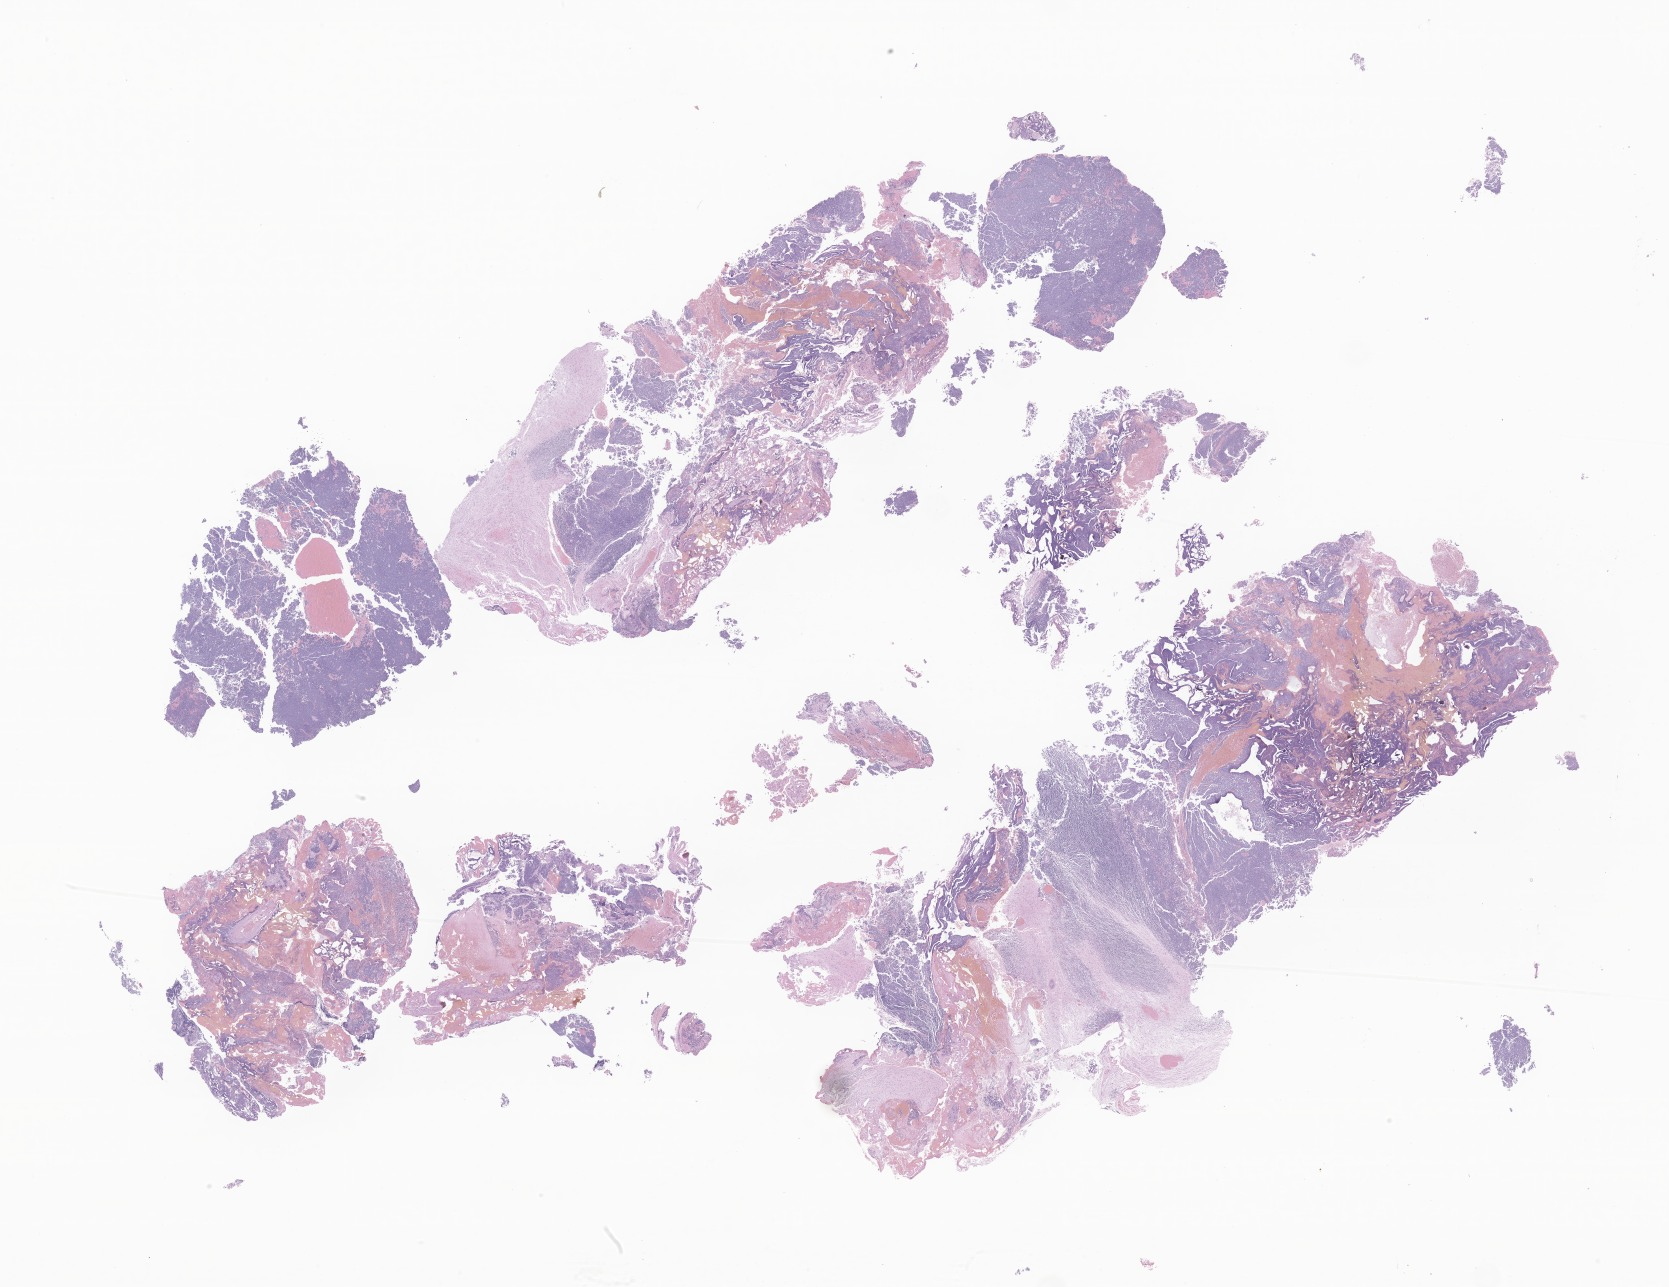
Digitized hematoxylin and eosin (H&E)-stained section of tumor tissue from the cerebellum, whole scanned area (about 28.1 x 21.7 mm) shown as a low-resolution overview, formalin-fixed paraffin-embedded section. Patient: female, age 121 months (10 years 1 month).
Diagnosis (ICD-O-3 morphology term): Ependymoma, NOS.